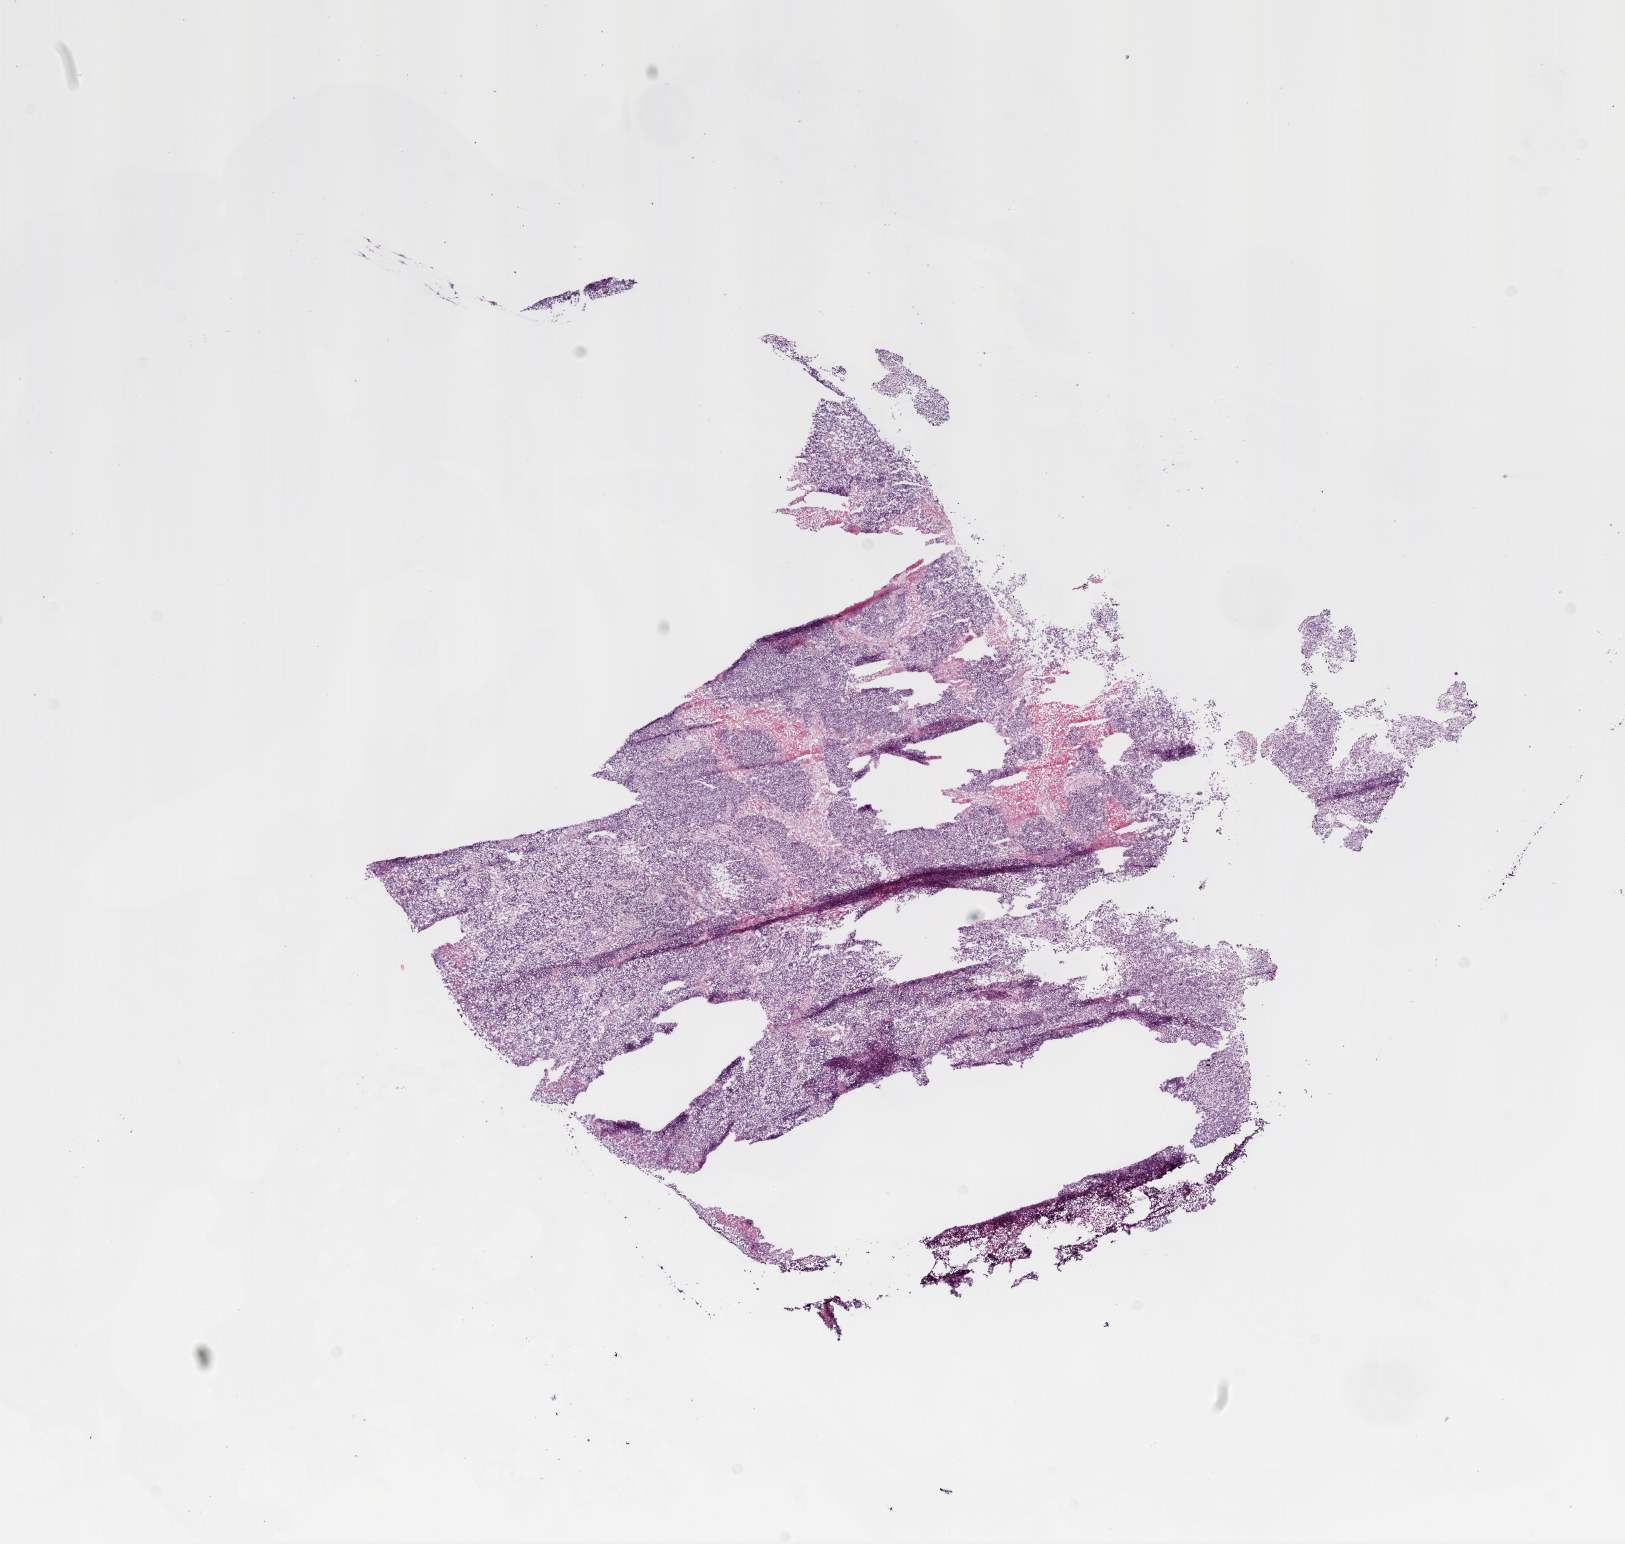
Digitized Hematoxylin and eosin (H&E) stained tissue section (whole slide) — whole scanned area (about 13.0 x 12.4 mm, from a 20x scan) shown as a low-resolution overview; frozen section from the bottom of the tissue portion; ovary, primary tumour sample. Female patient; age at initial diagnosis 58 years. Histologic grade: G3 (poorly differentiated). Pathologist review of this section (percent, as recorded): tumour cells 85%, tumour nuclei 95%, normal cells 0%, stromal cells 5%, necrosis 10%.
Histologic diagnosis: Serous cystadenocarcinoma, NOS. FIGO stage: IIIC.